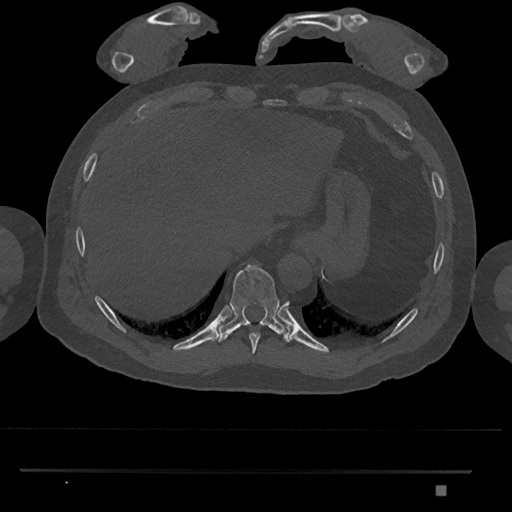
CT including the spine, one axial slice; position 1018 of 1134 along the scan axis; 120 kVp; bone window (W 1800 / L 400 HU); 0.5 mm slice thickness; 512 × 512 image matrix, field of view 429 × 429 mm. Male patient, age 65 years. From the clinical record (not read from this slice): primary cancer: prostate.
Structures marked on this image (semi-automatic segmentation, software-assisted and operator-edited):
- T10 vertebra: bounding box <216,264,289,343> (left, top, right, bottom; pixels)
- T9 vertebra: <249,333,260,354>